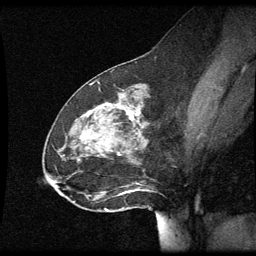
Breast MRI (dynamic contrast-enhanced), one sagittal slice. Slice 27 of 60 in the series (ordered by position). Dynamic contrast-enhanced series, image 2 of 3 at this slice position (ordered by acquisition). 1.5 T. TE 4.2 ms, TR 8.9 ms. 2 mm slice thickness. 256 × 256 image matrix. Patient: female, 49 years. From the clinical record (not read from this slice): setting: breast cancer imaged before/during neoadjuvant chemotherapy; receptor status: HR-positive, HER2-negative.
Annotated regions visible in this slice (semi-automatically segmented with operator editing):
- analysis volume of interest (the breast-tissue region the enhancement analysis was run in; not a lesion): bounding box <46,92,151,205> (left, top, right, bottom; pixels)
- tumour enhancement mask (voxels above the 70 % enhancement threshold inside the analysis volume of interest): <117,104,141,121>